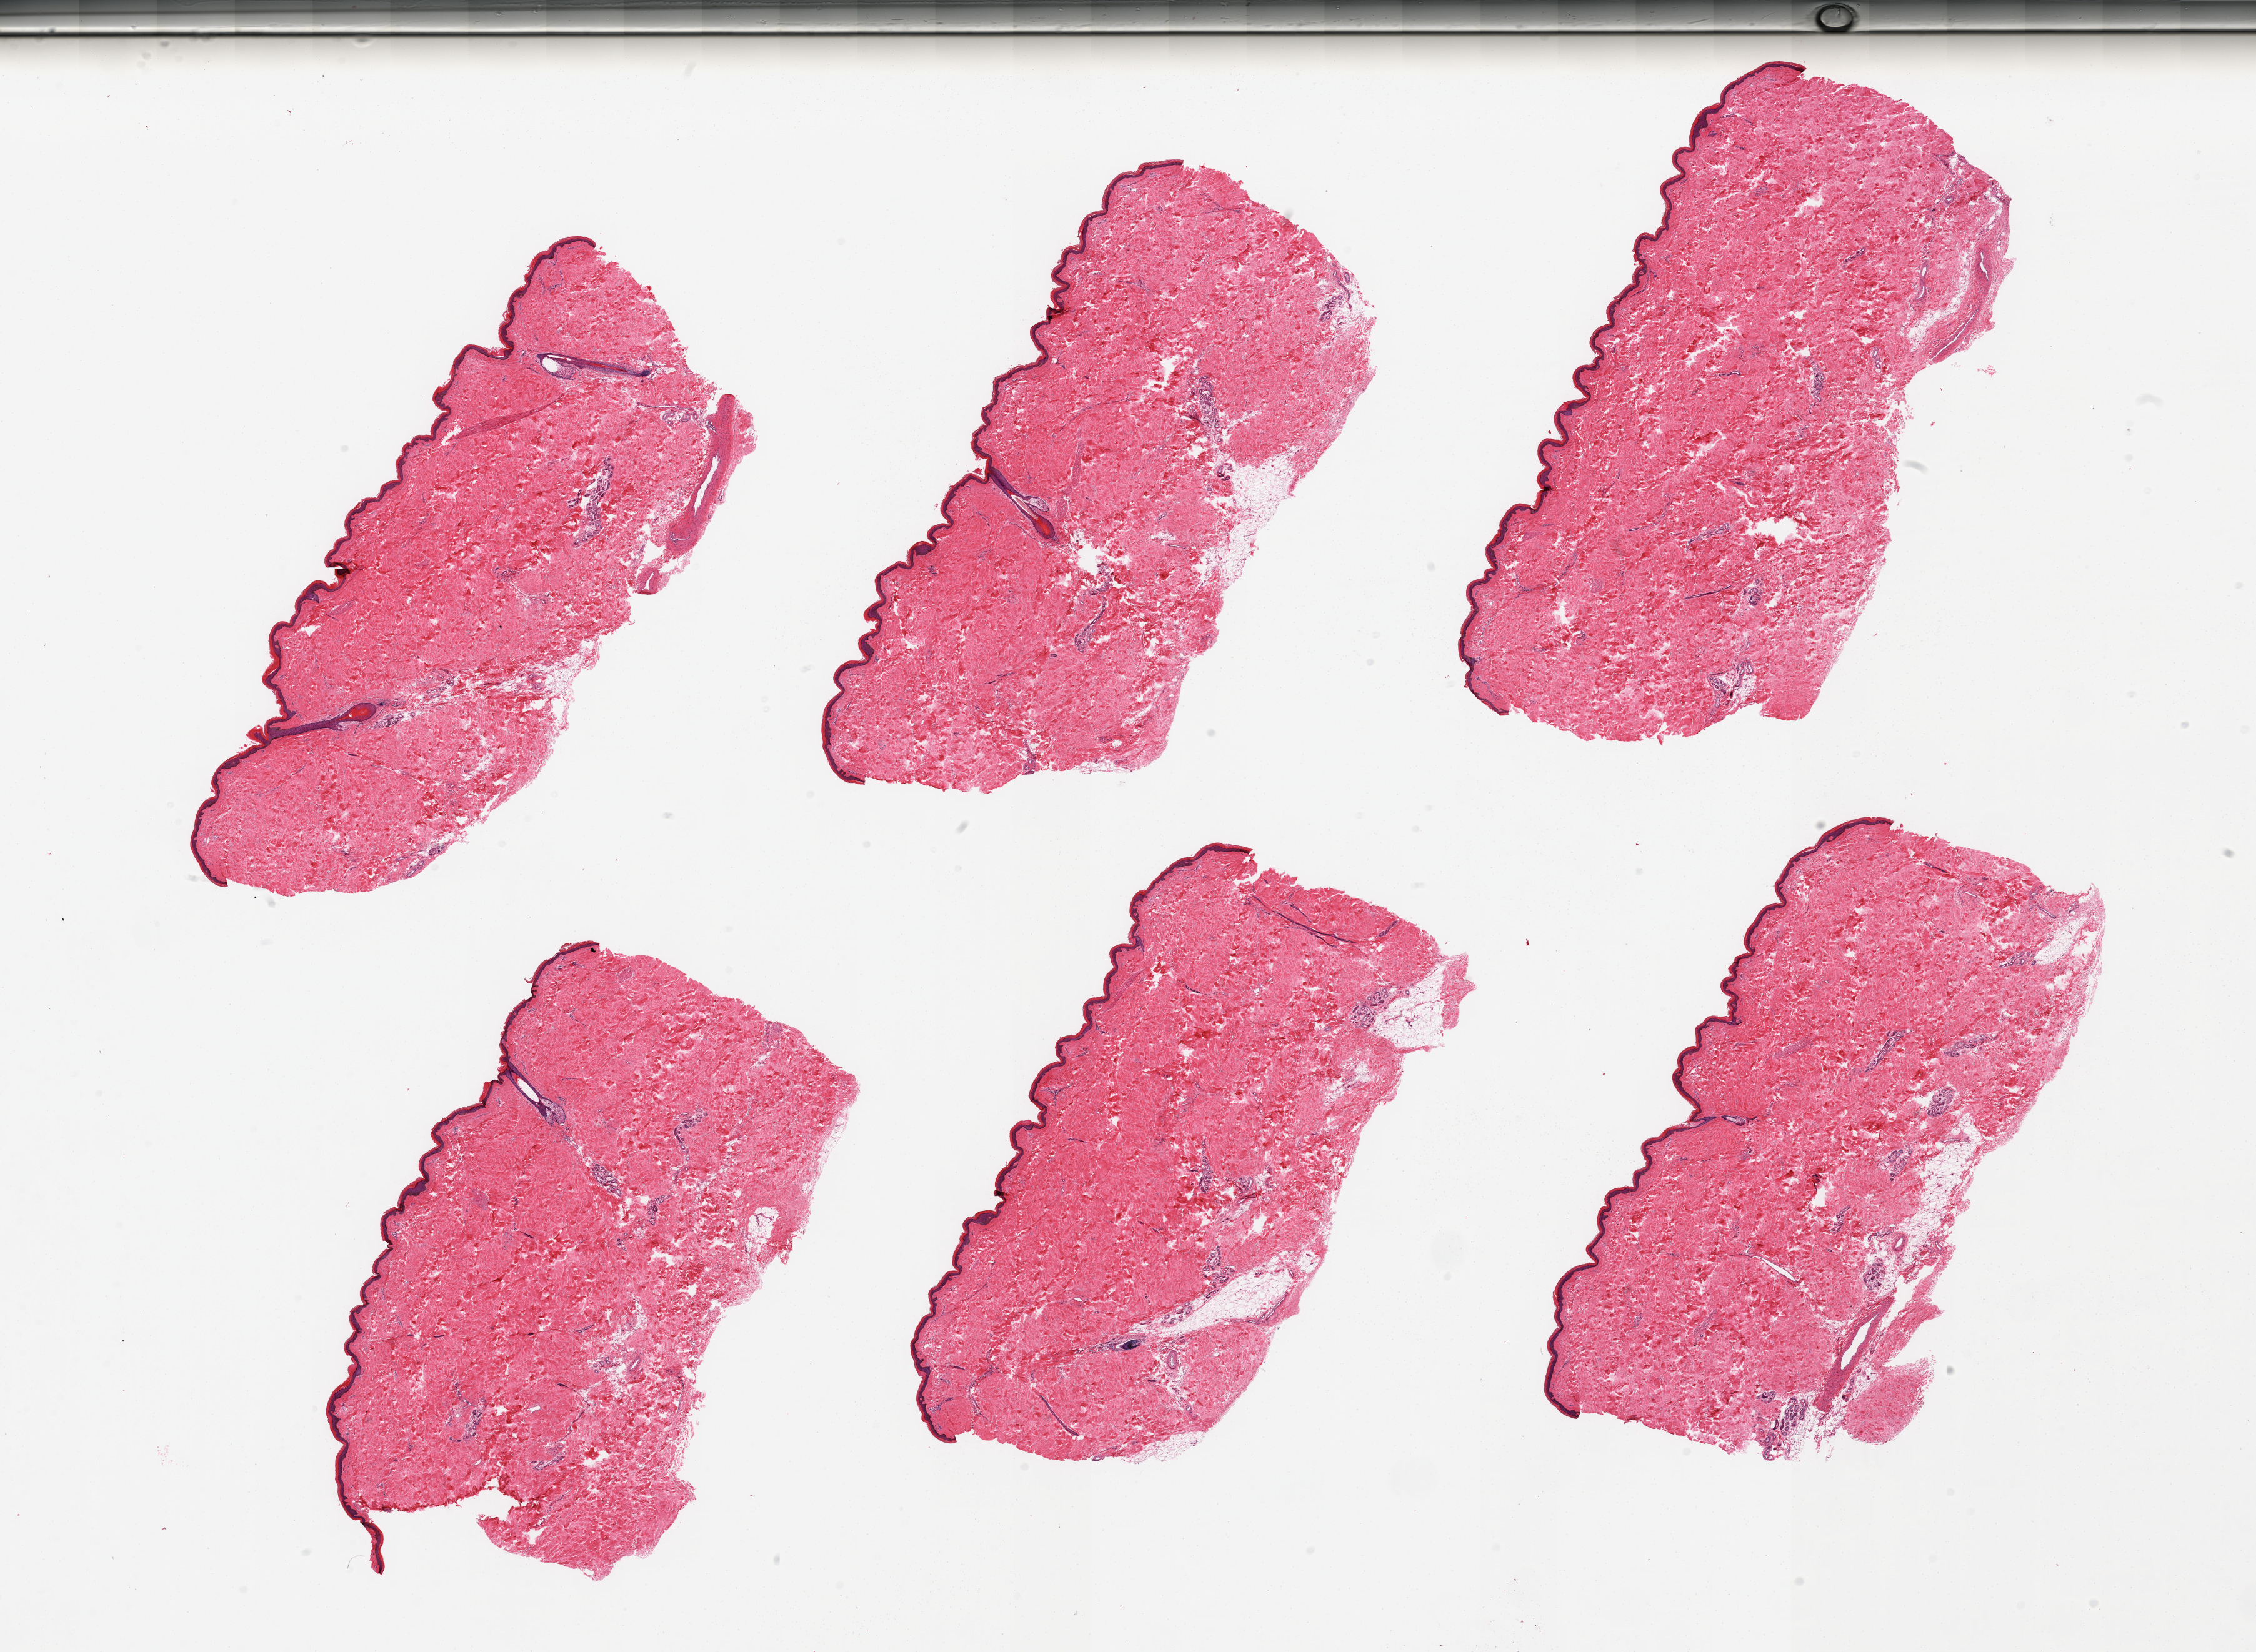
Haematoxylin and eosin whole-slide image, brightfield — low-resolution overview of the scanned area, about 28.5 x 20.9 mm, PAXgene-fixed, paraffin-embedded tissue, section of skin of lower leg (target tissue), donor tissue sample. Male donor.
- review note (as recorded): 6 pieces, trace dermal fat; squamous epithelium is ~30-40 microns